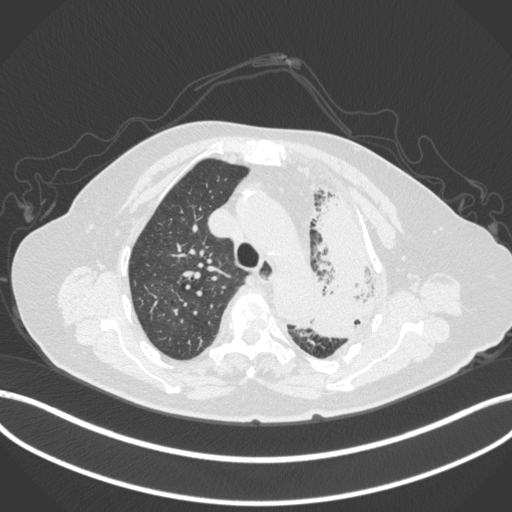
Chest CT, one axial slice. Slice 292 of 399 in the series (ordered by position). 120 kVp. Lung window (W 1500 / L -600 HU). 1 mm slice thickness. 512 × 512 image matrix. Female patient, age 75 years. Case-level facts recorded for this patient, not image findings: clinical TNM (as recorded): T3 N3 M1.
Annotated regions visible in this slice (rectangle marked by the reading radiologist):
- lung tumour (recorded histology: adenocarcinoma): bounding box [x1, y1, x2, y2] px = [308, 189, 387, 341]